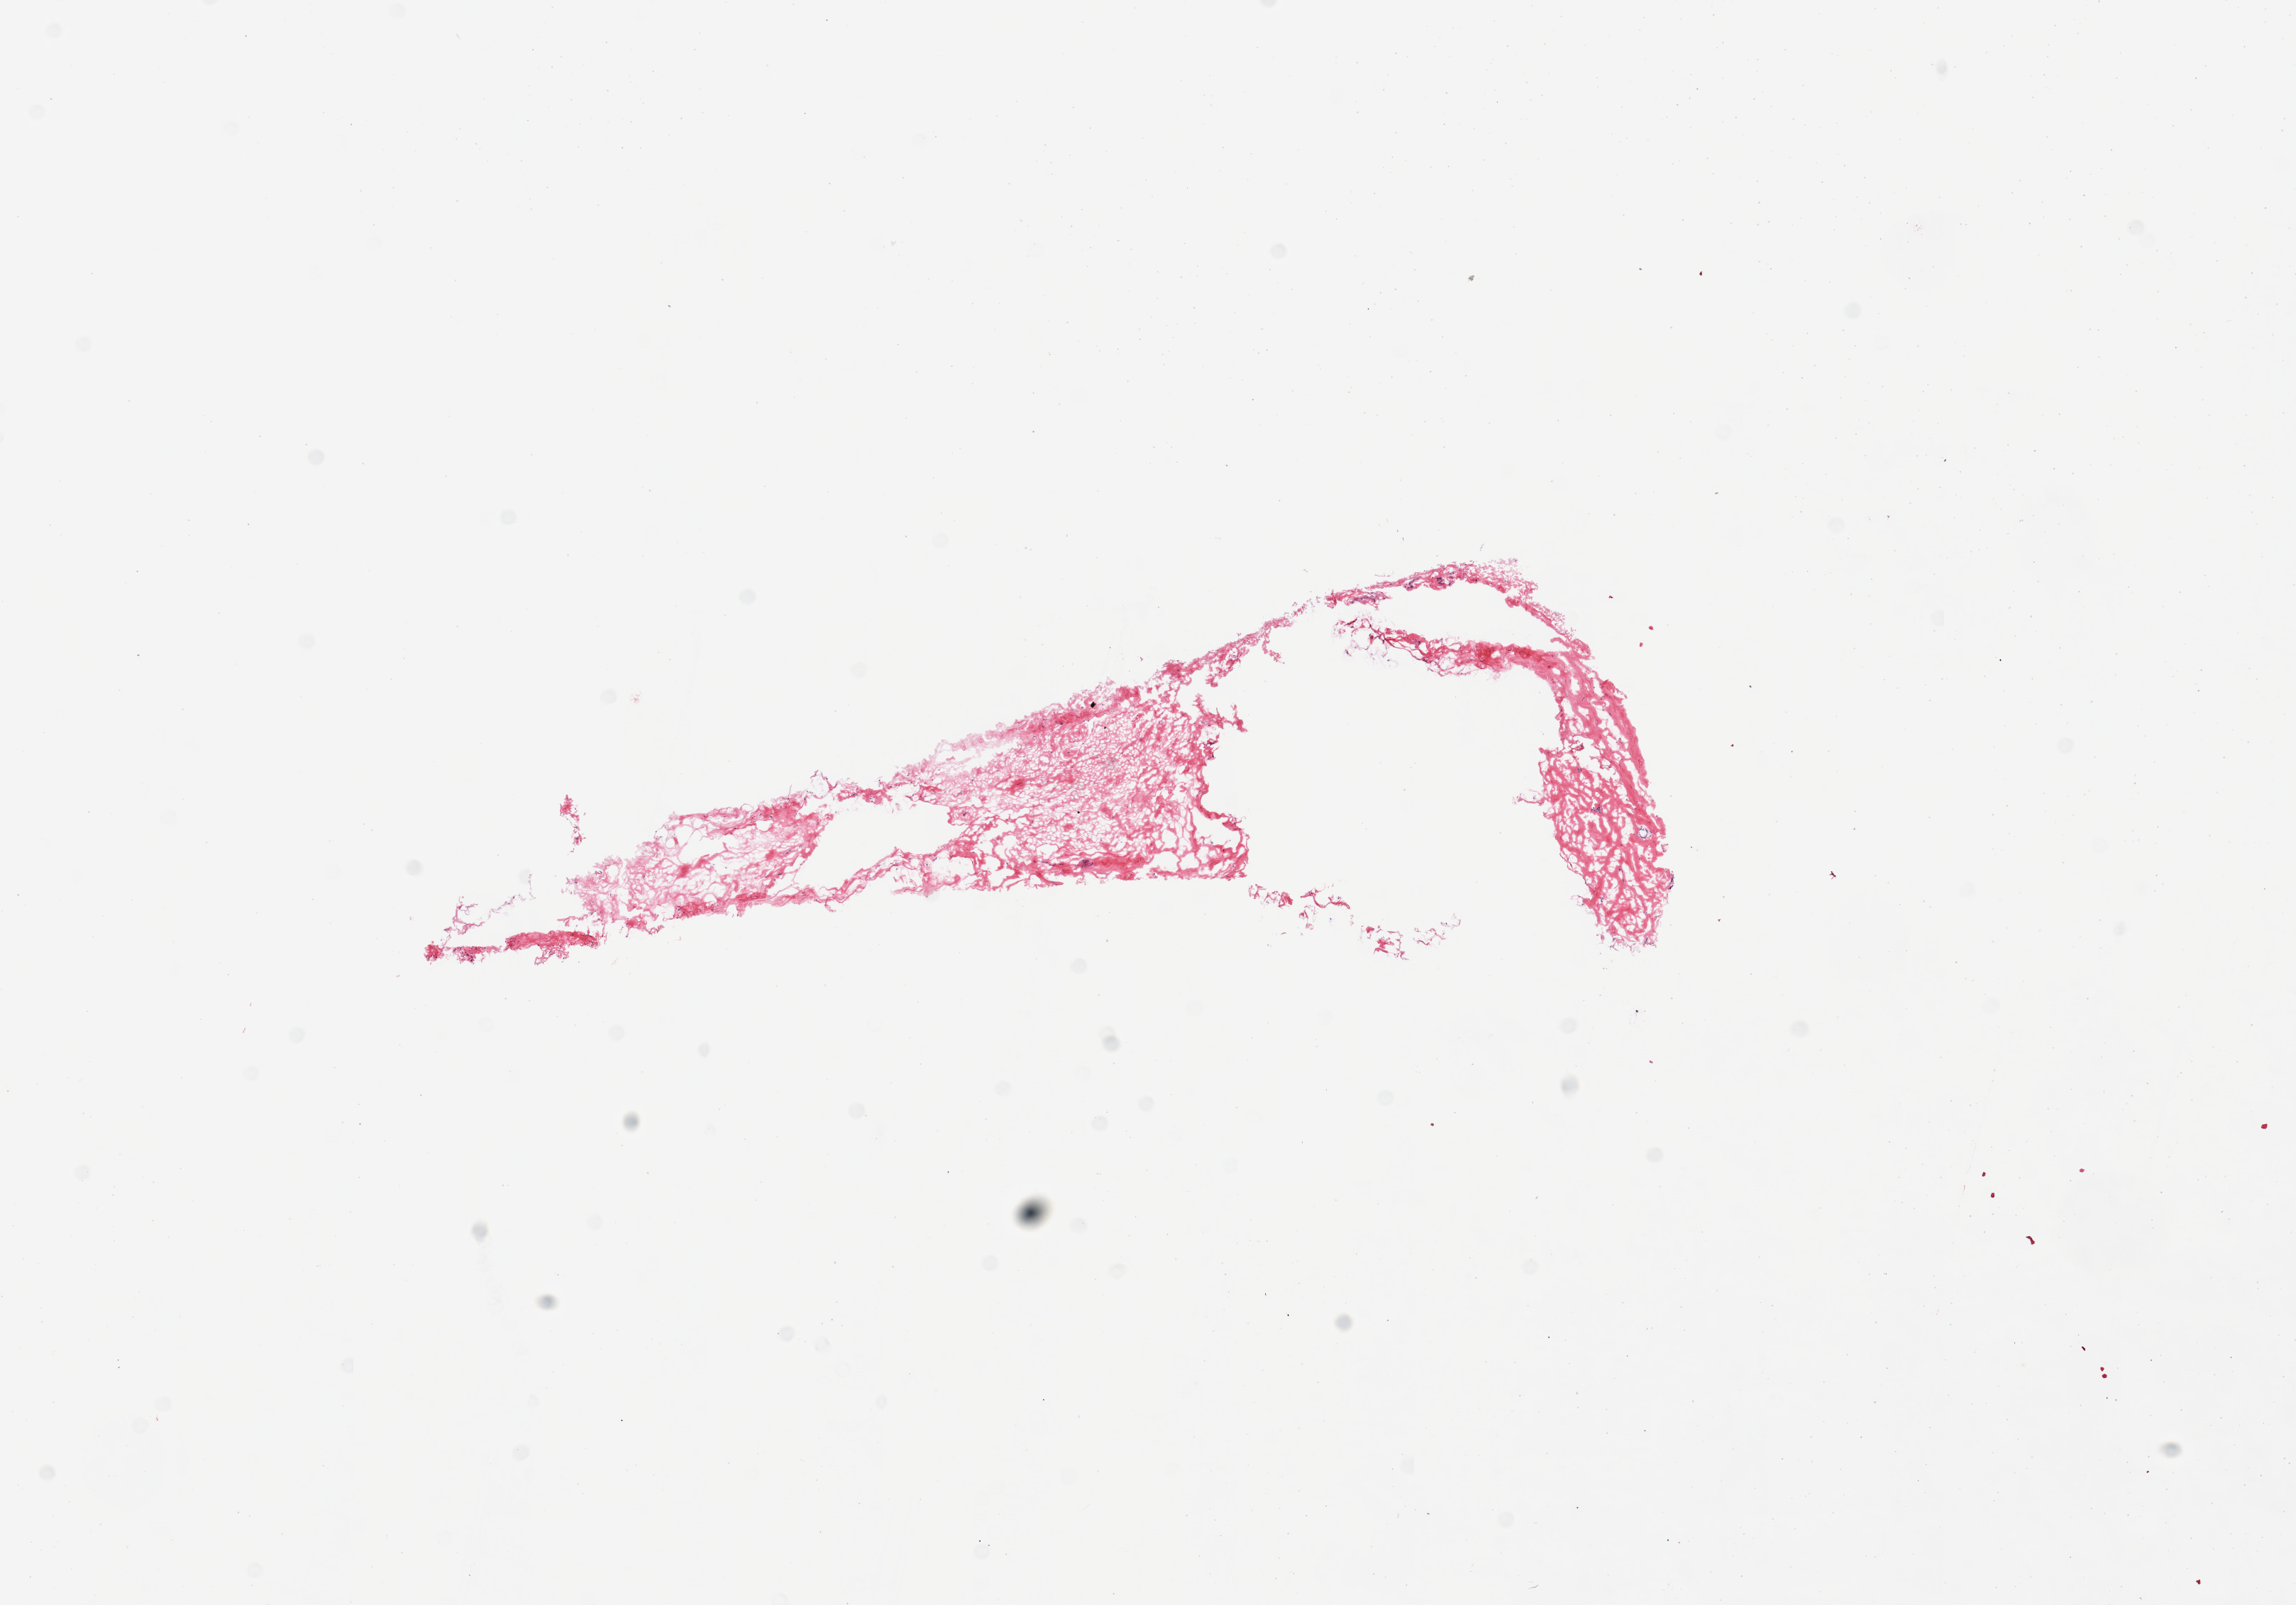
Digitized H&E-stained section, low-resolution overview of the scanned area, about 12.8 x 8.9 mm (slide scanned at 20x). Donor sex: female.
Specimen: frozen section (dry ice); section of breast (target tissue); donor tissue sample.